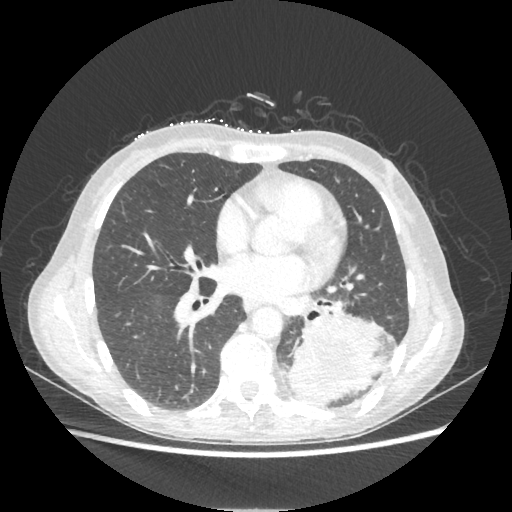
Chest CT, one axial slice. Position 105 of 221 along the scan axis. Reconstruction kernel STANDARD. 80 kVp. Lung window (W 1500 / L -600 HU). 1.25 mm slice thickness. 512 × 512 image matrix, field of view 360 × 360 mm. Female patient, age 53 years. From the clinical record (not read from this slice): clinical TNM (as recorded): T3 N0 M0.
Annotated regions visible in this slice (bounding box drawn by a radiologist):
- lung tumour (recorded histology: adenocarcinoma): bounding box [x1, y1, x2, y2] px = [287, 312, 388, 403]